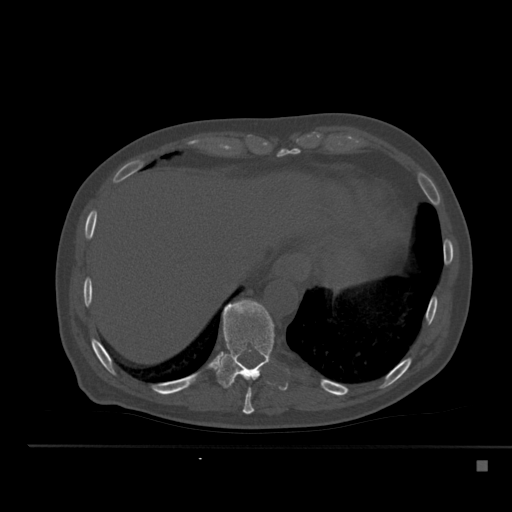
CT including the spine, one axial slice; position 271 of 517 along the scan axis; reconstruction kernel Br40s; 120 kVp; bone window (W 1800 / L 400 HU); 1.5 mm slice thickness; 512 × 512 image matrix, field of view 408 × 408 mm. Male patient, age 70 years. Case-level facts recorded for this patient, not image findings: primary cancer: renal; vertebrae with lytic lesions (as recorded): T4, T6, T10, T12, L3, L4, L5.
Outlined on this slice (semi-automatic segmentation, software-assisted and operator-edited):
- T10 vertebra: box from (x=217, y=300) to (x=275, y=388) px
- T9 vertebra: (x=243, y=388)–(x=254, y=414)